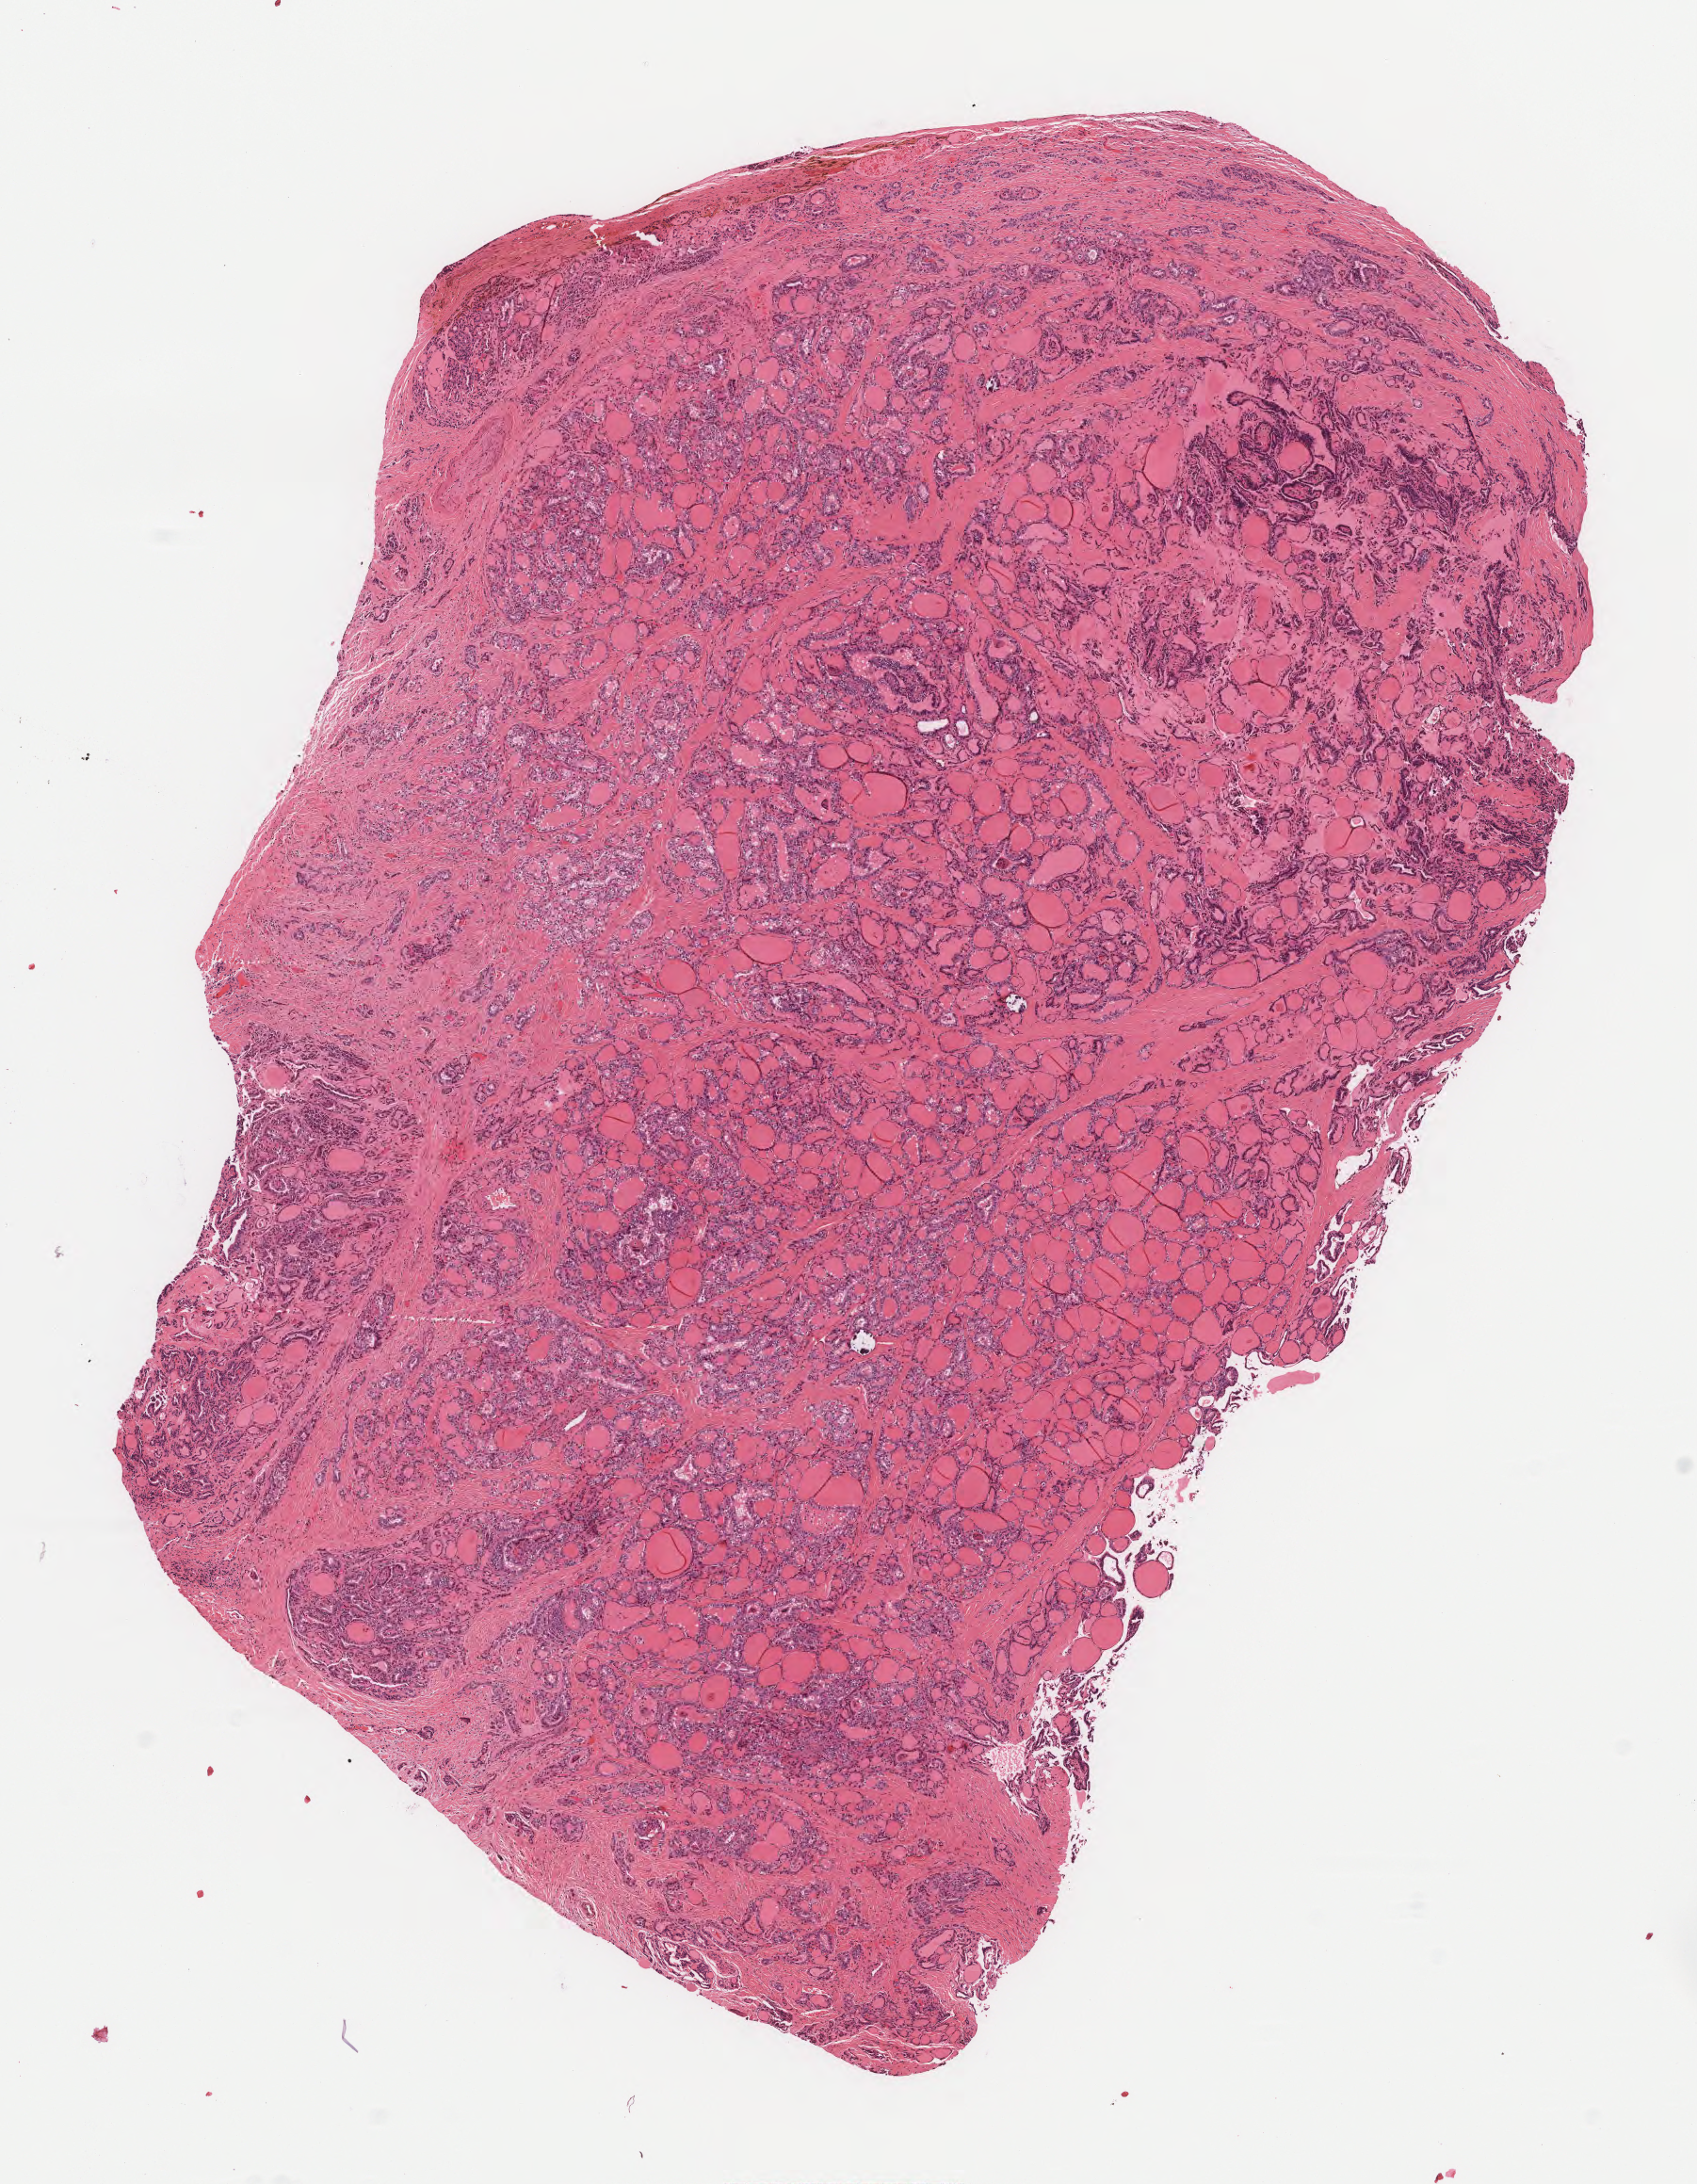
Digitized H&E tissue section (whole slide), shown as a low-resolution overview of the whole scanned area (about 7.3 x 9.3 mm, from a 40x scan), formalin-fixed paraffin-embedded (FFPE) diagnostic section, thyroid, primary tumour sample. Female, age 36 years at initial diagnosis.
AJCC pathologic stage: I (7th edition). Lymph nodes positive (case pathology): 27 of 80 examined. Histologic diagnosis: Papillary adenocarcinoma, NOS (thyroid gland). TNM: T1b N1b MX. Laterality: right.